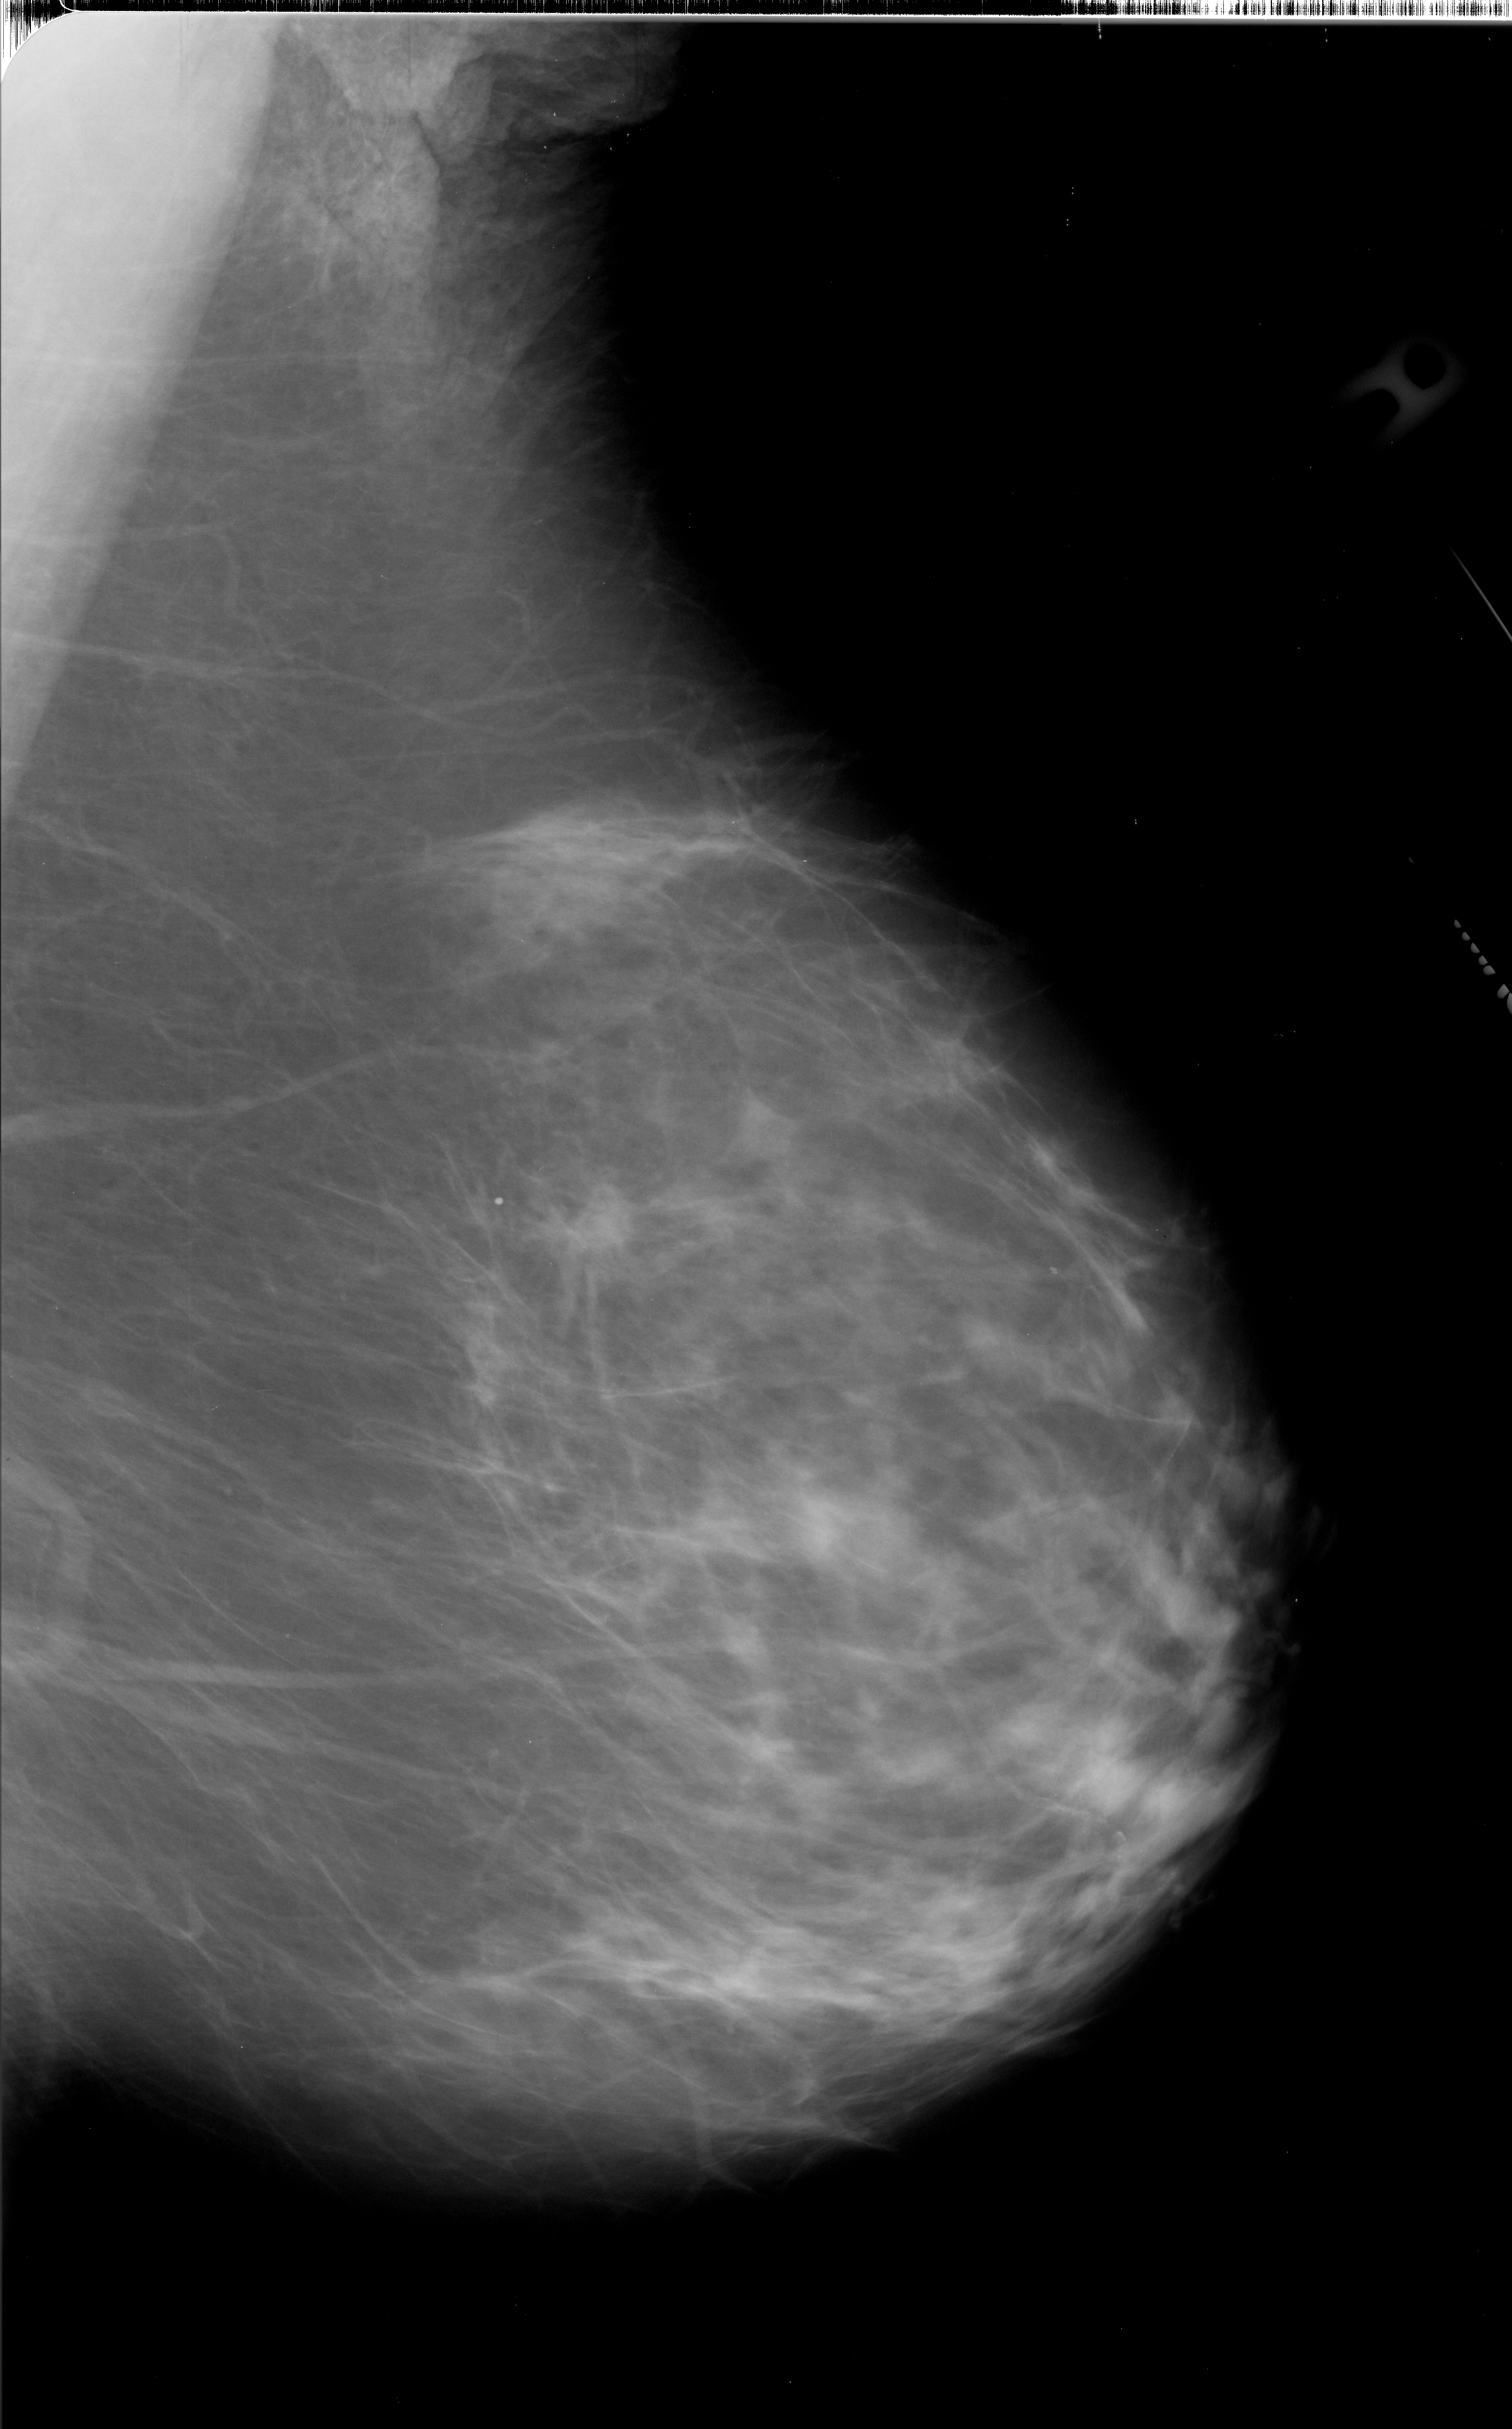
Mammogram (digitized film); right breast; mediolateral oblique (MLO) view; breast composition: scattered fibroglandular densities (BI-RADS density category 2 of 4); 1512 × 2429 image matrix.
Marked abnormalities (boxes around the expert regions of interest):
- mass, shape irregular, margins spiculated; BI-RADS assessment category 5; pathology result (as recorded, not read from the image): malignant: bounding box <550,1163,678,1262> (left, top, right, bottom; pixels)